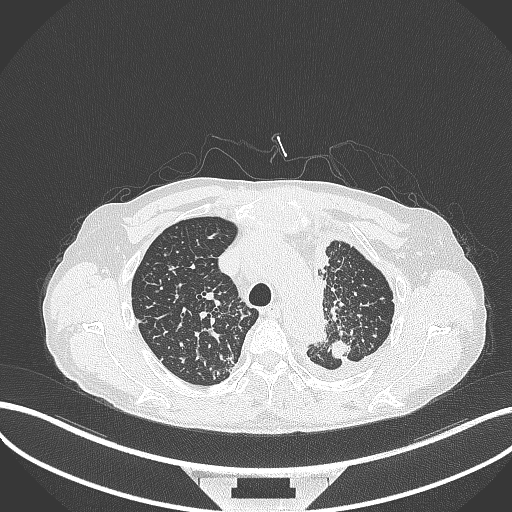
Chest CT, one axial slice. Position 272 of 325 along the scan axis. Lung window (W 1500 / L -600 HU). 1 mm slice thickness. 512 × 512 image matrix, field of view 400 × 400 mm. Male patient, age 58 years. From the clinical record (not read from this slice): clinical TNM (as recorded): T1c N3 M1.
Outlined on this slice (bounding box drawn by a radiologist):
- lung tumour (recorded histology: adenocarcinoma): bounding box <328,339,354,361> (left, top, right, bottom; pixels)